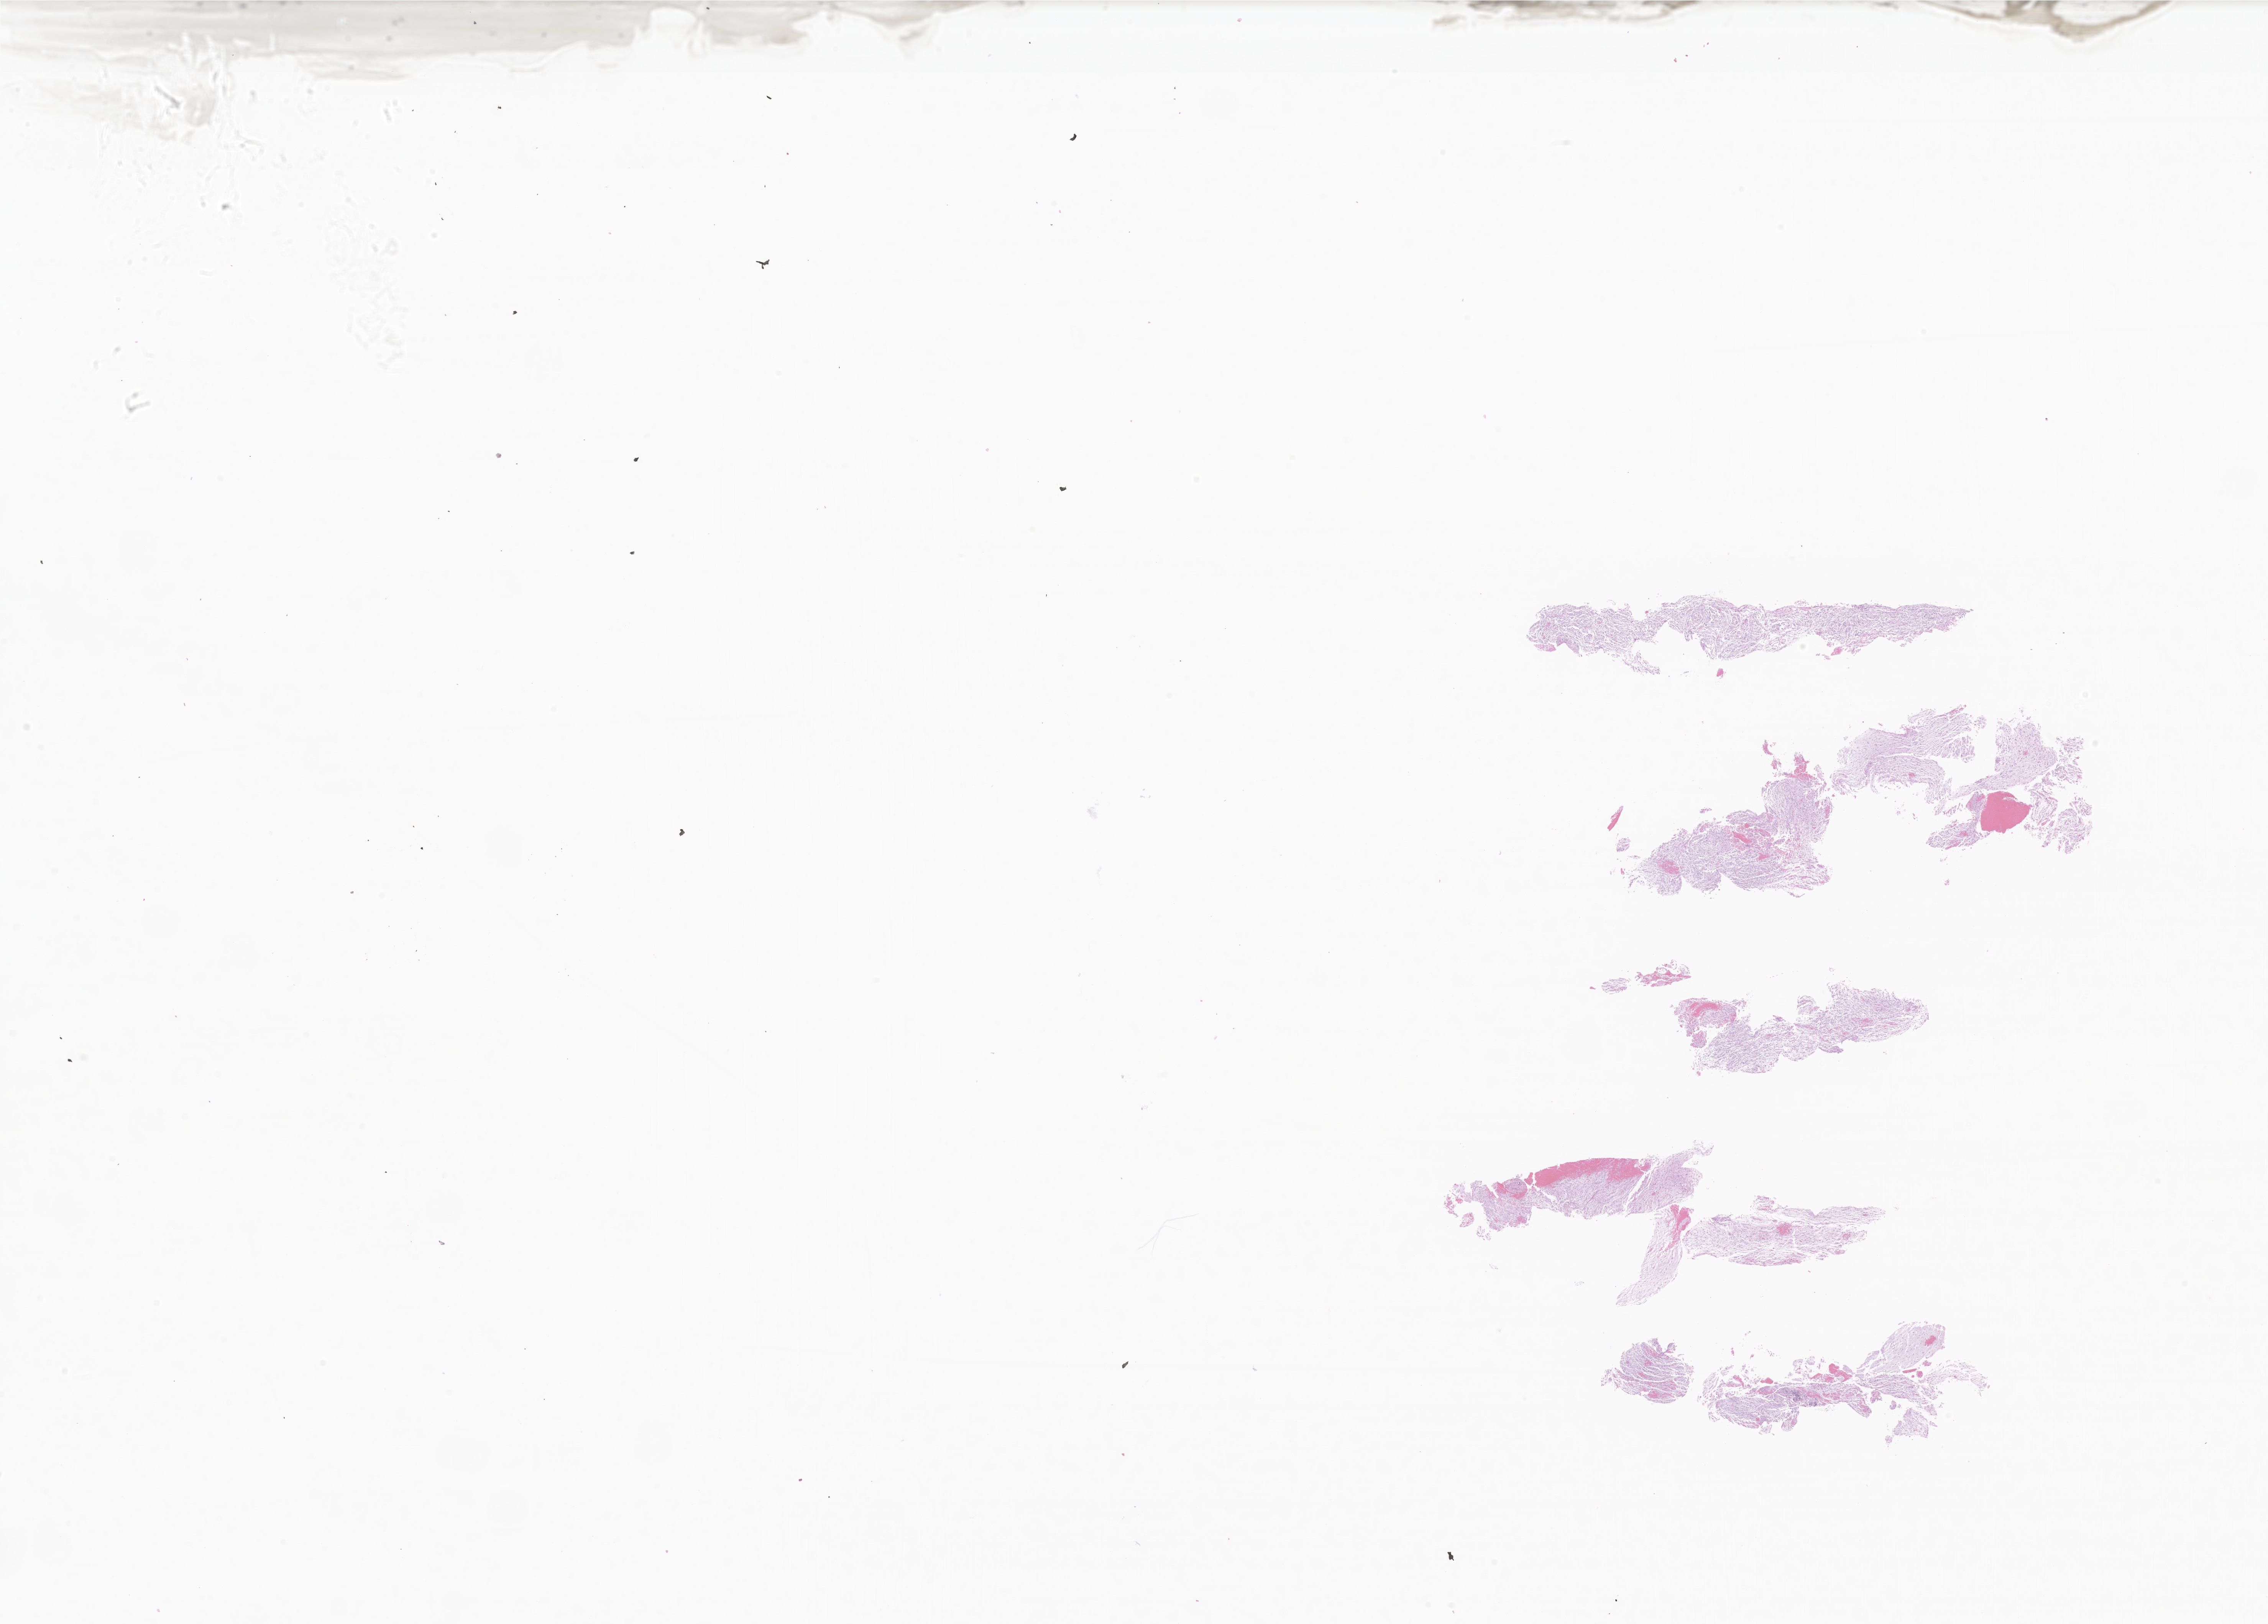
Whole-slide image, haematoxylin and eosin stain of tumor tissue from the brain — low-resolution overview of the scanned area, about 24.9 x 17.9 mm, formalin-fixed, paraffin-embedded (FFPE) tissue. Patient: male, age 92 days.
• diagnosis: Neoplasm, uncertain whether benign or malignant